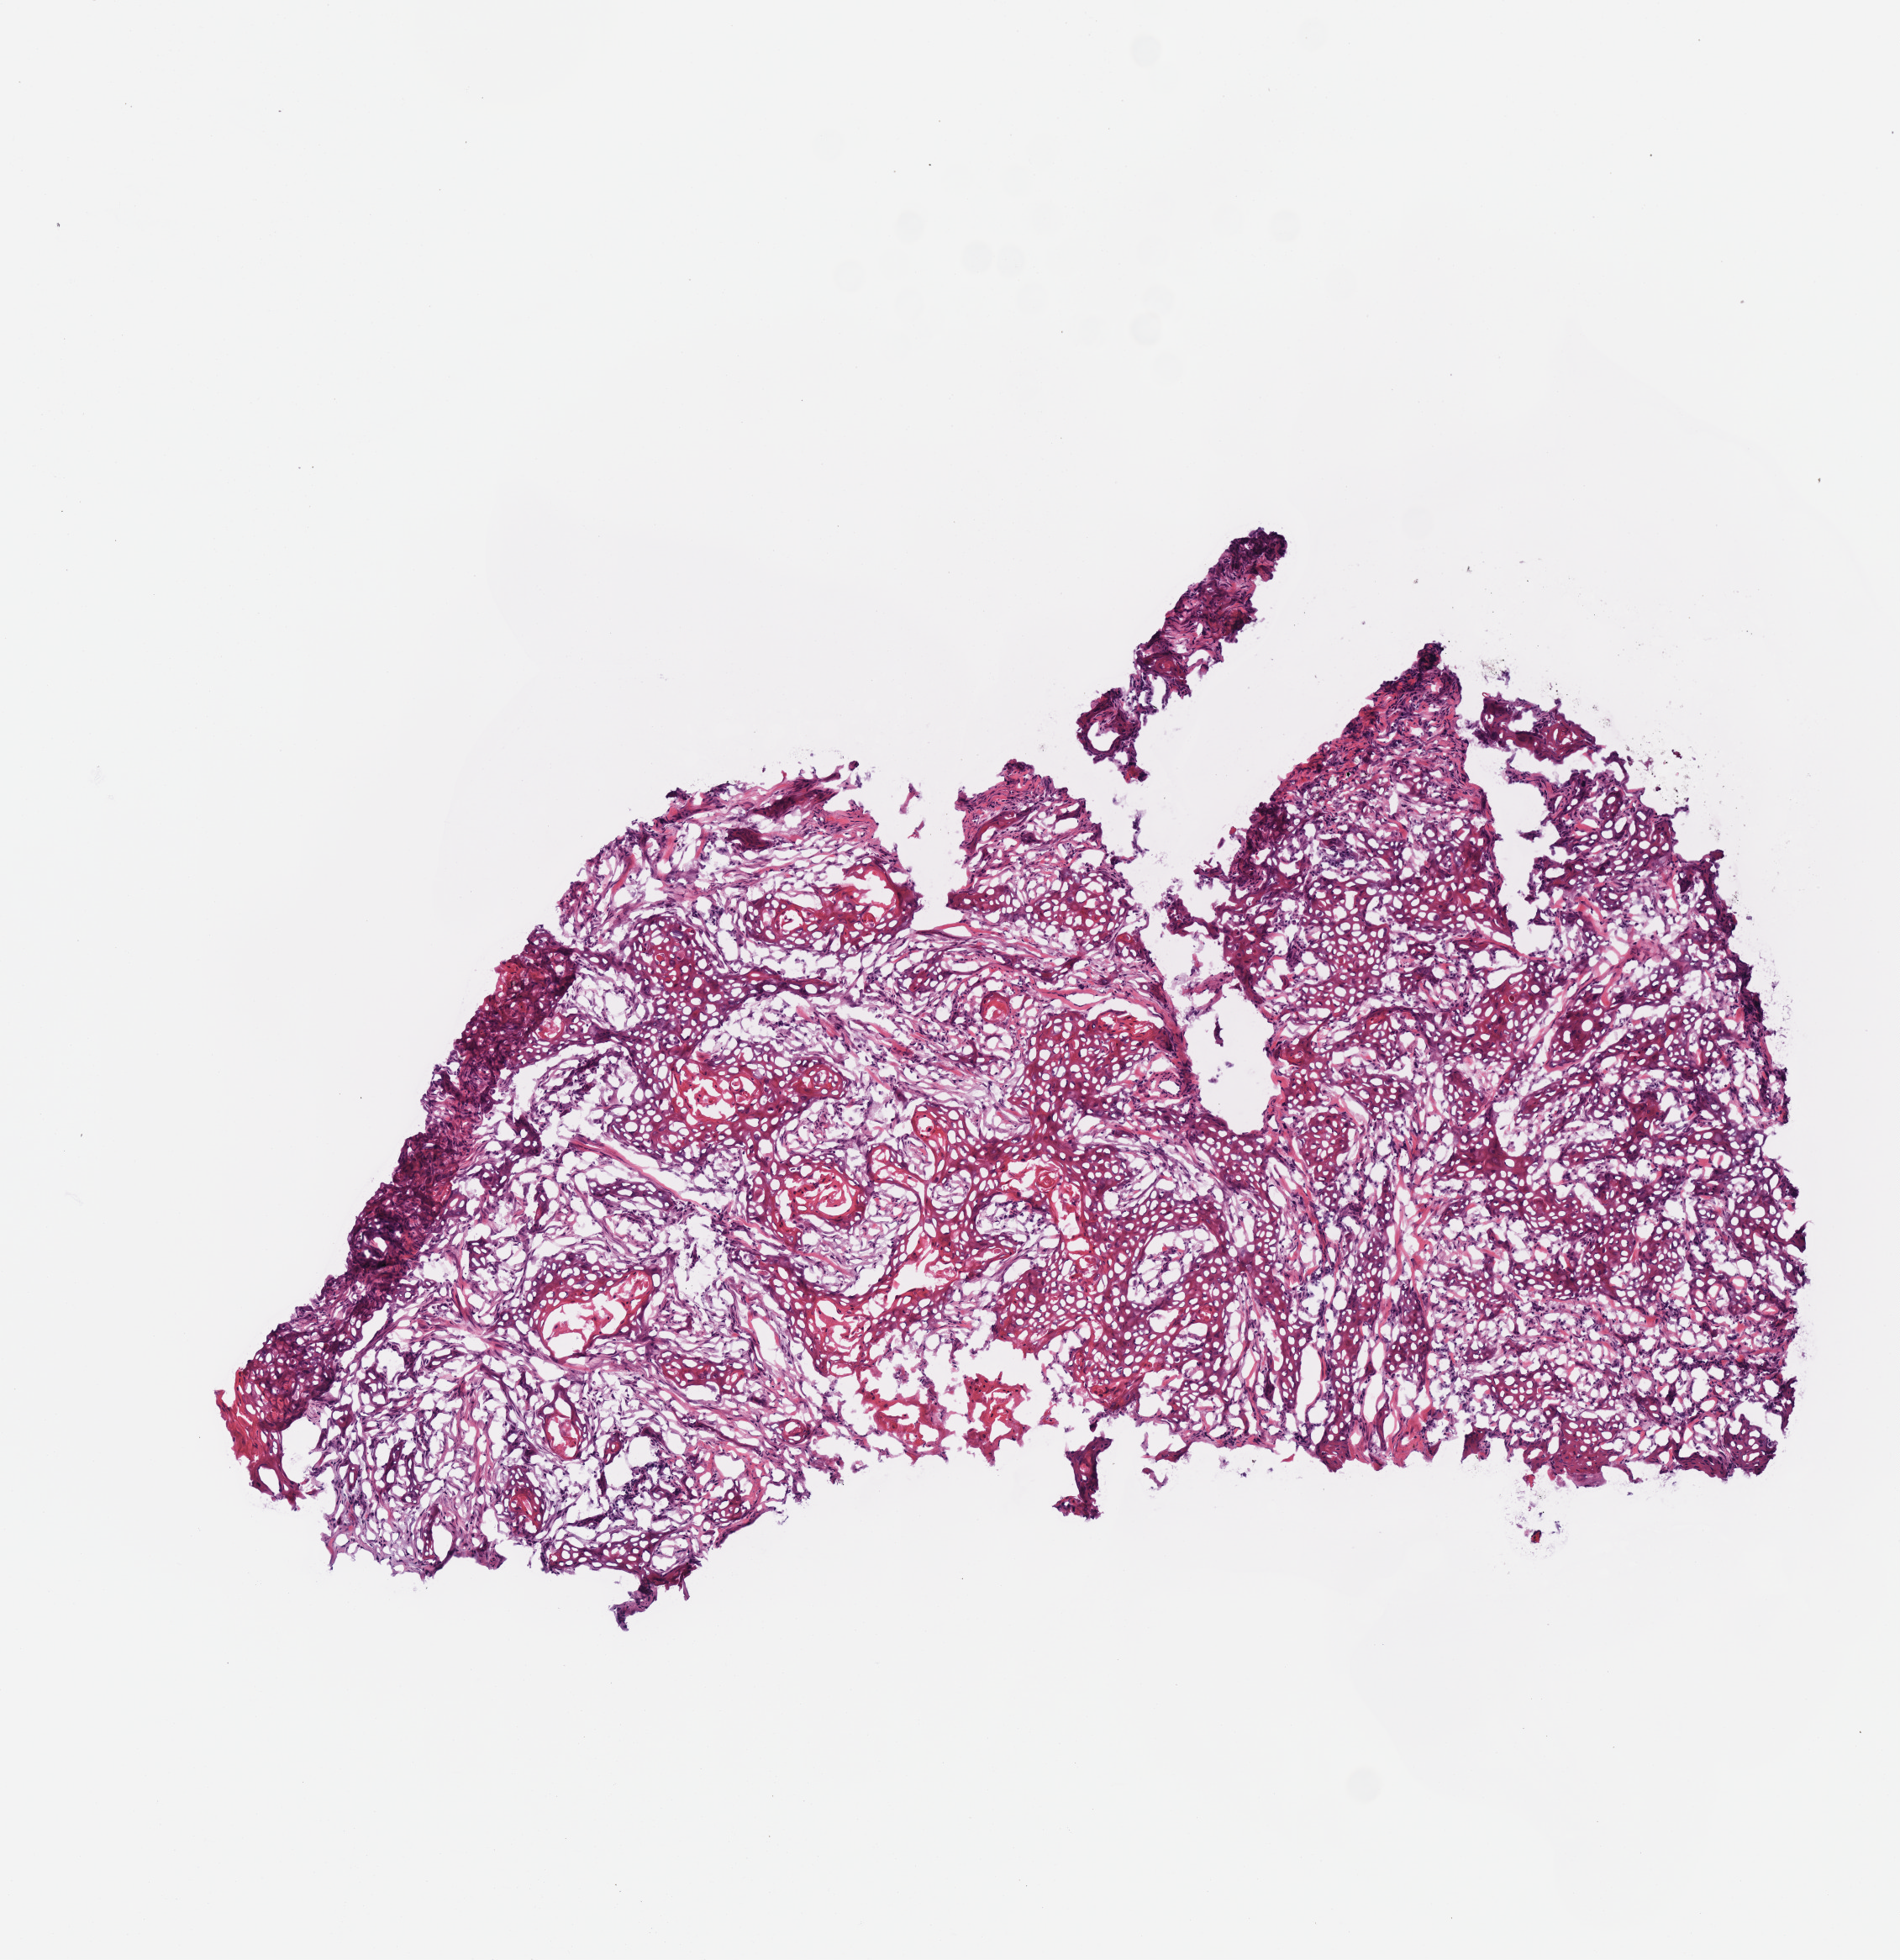
Digitized Hematoxylin and eosin (H&E) stained tissue section (whole slide), low-resolution overview of the scanned area, about 4.5 x 4.6 mm (from a 40x scan); frozen section from the top of the tissue portion; head and neck, primary tumour sample. Male, age 60 years at initial diagnosis. Pathologist review of this section (percent, as recorded): tumour cells 100%, tumour nuclei 75%.
Histologic diagnosis: Squamous cell carcinoma, NOS (larynx, NOS).